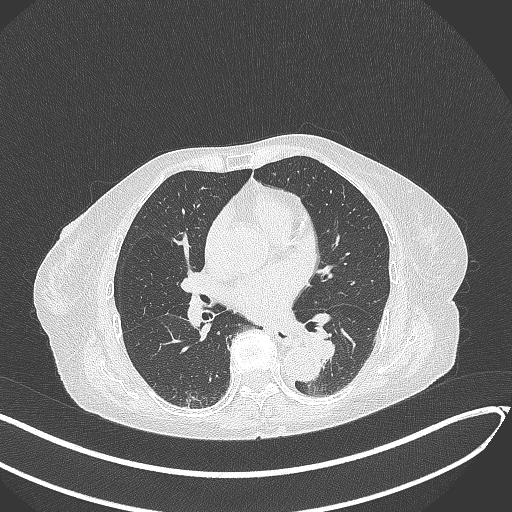
Chest CT, one axial slice; position 123 of 324 along the scan axis; 120 kVp; lung window (W 1500 / L -600 HU); 512 × 512 image matrix. Female patient, age 82 years. From the clinical record (not read from this slice): clinical TNM (as recorded): T1b N0 M1.
Annotated regions visible in this slice (bounding box drawn by a radiologist):
- lung tumour (recorded histology: adenocarcinoma): bounding box (x1, y1, x2, y2) in pixels: (303, 330, 340, 366)